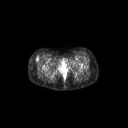
FDG PET of an extremity soft-tissue mass (from a PET/CT study), one axial slice; slice 49 of 267 in the series (ordered by position); 3.27 mm slice thickness; 128 × 128 image matrix. Female patient, age 34 years. From the clinical record (not read from this slice): histological type: synovial sarcoma; grade: intermediate; site of the primary tumour: right thigh.
Annotated regions visible in this slice (expert contour drawn on MRI and transferred to this co-registered scan by the dataset authors):
- gross tumour volume including surrounding oedema: bounding box (x1, y1, x2, y2) in pixels: (35, 58, 38, 61)
- gross tumour volume (mass): (35, 58, 38, 61)